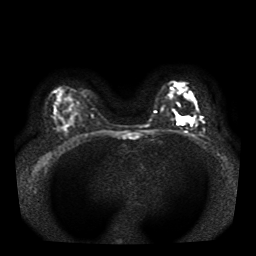
Breast MRI, one axial slice. Position 24 of 41 along the scan axis. Diffusion-weighted series; image 2 of 4 stored at this slice position (different b-values; order by instance number). 1.5 T. 5 mm slice thickness. 256 × 256 image matrix, field of view 330 × 330 mm. Female patient.
Structures marked on this image (outlined manually by an expert reader):
- tumour on diffusion-weighted imaging: box from (x=179, y=117) to (x=193, y=125) px